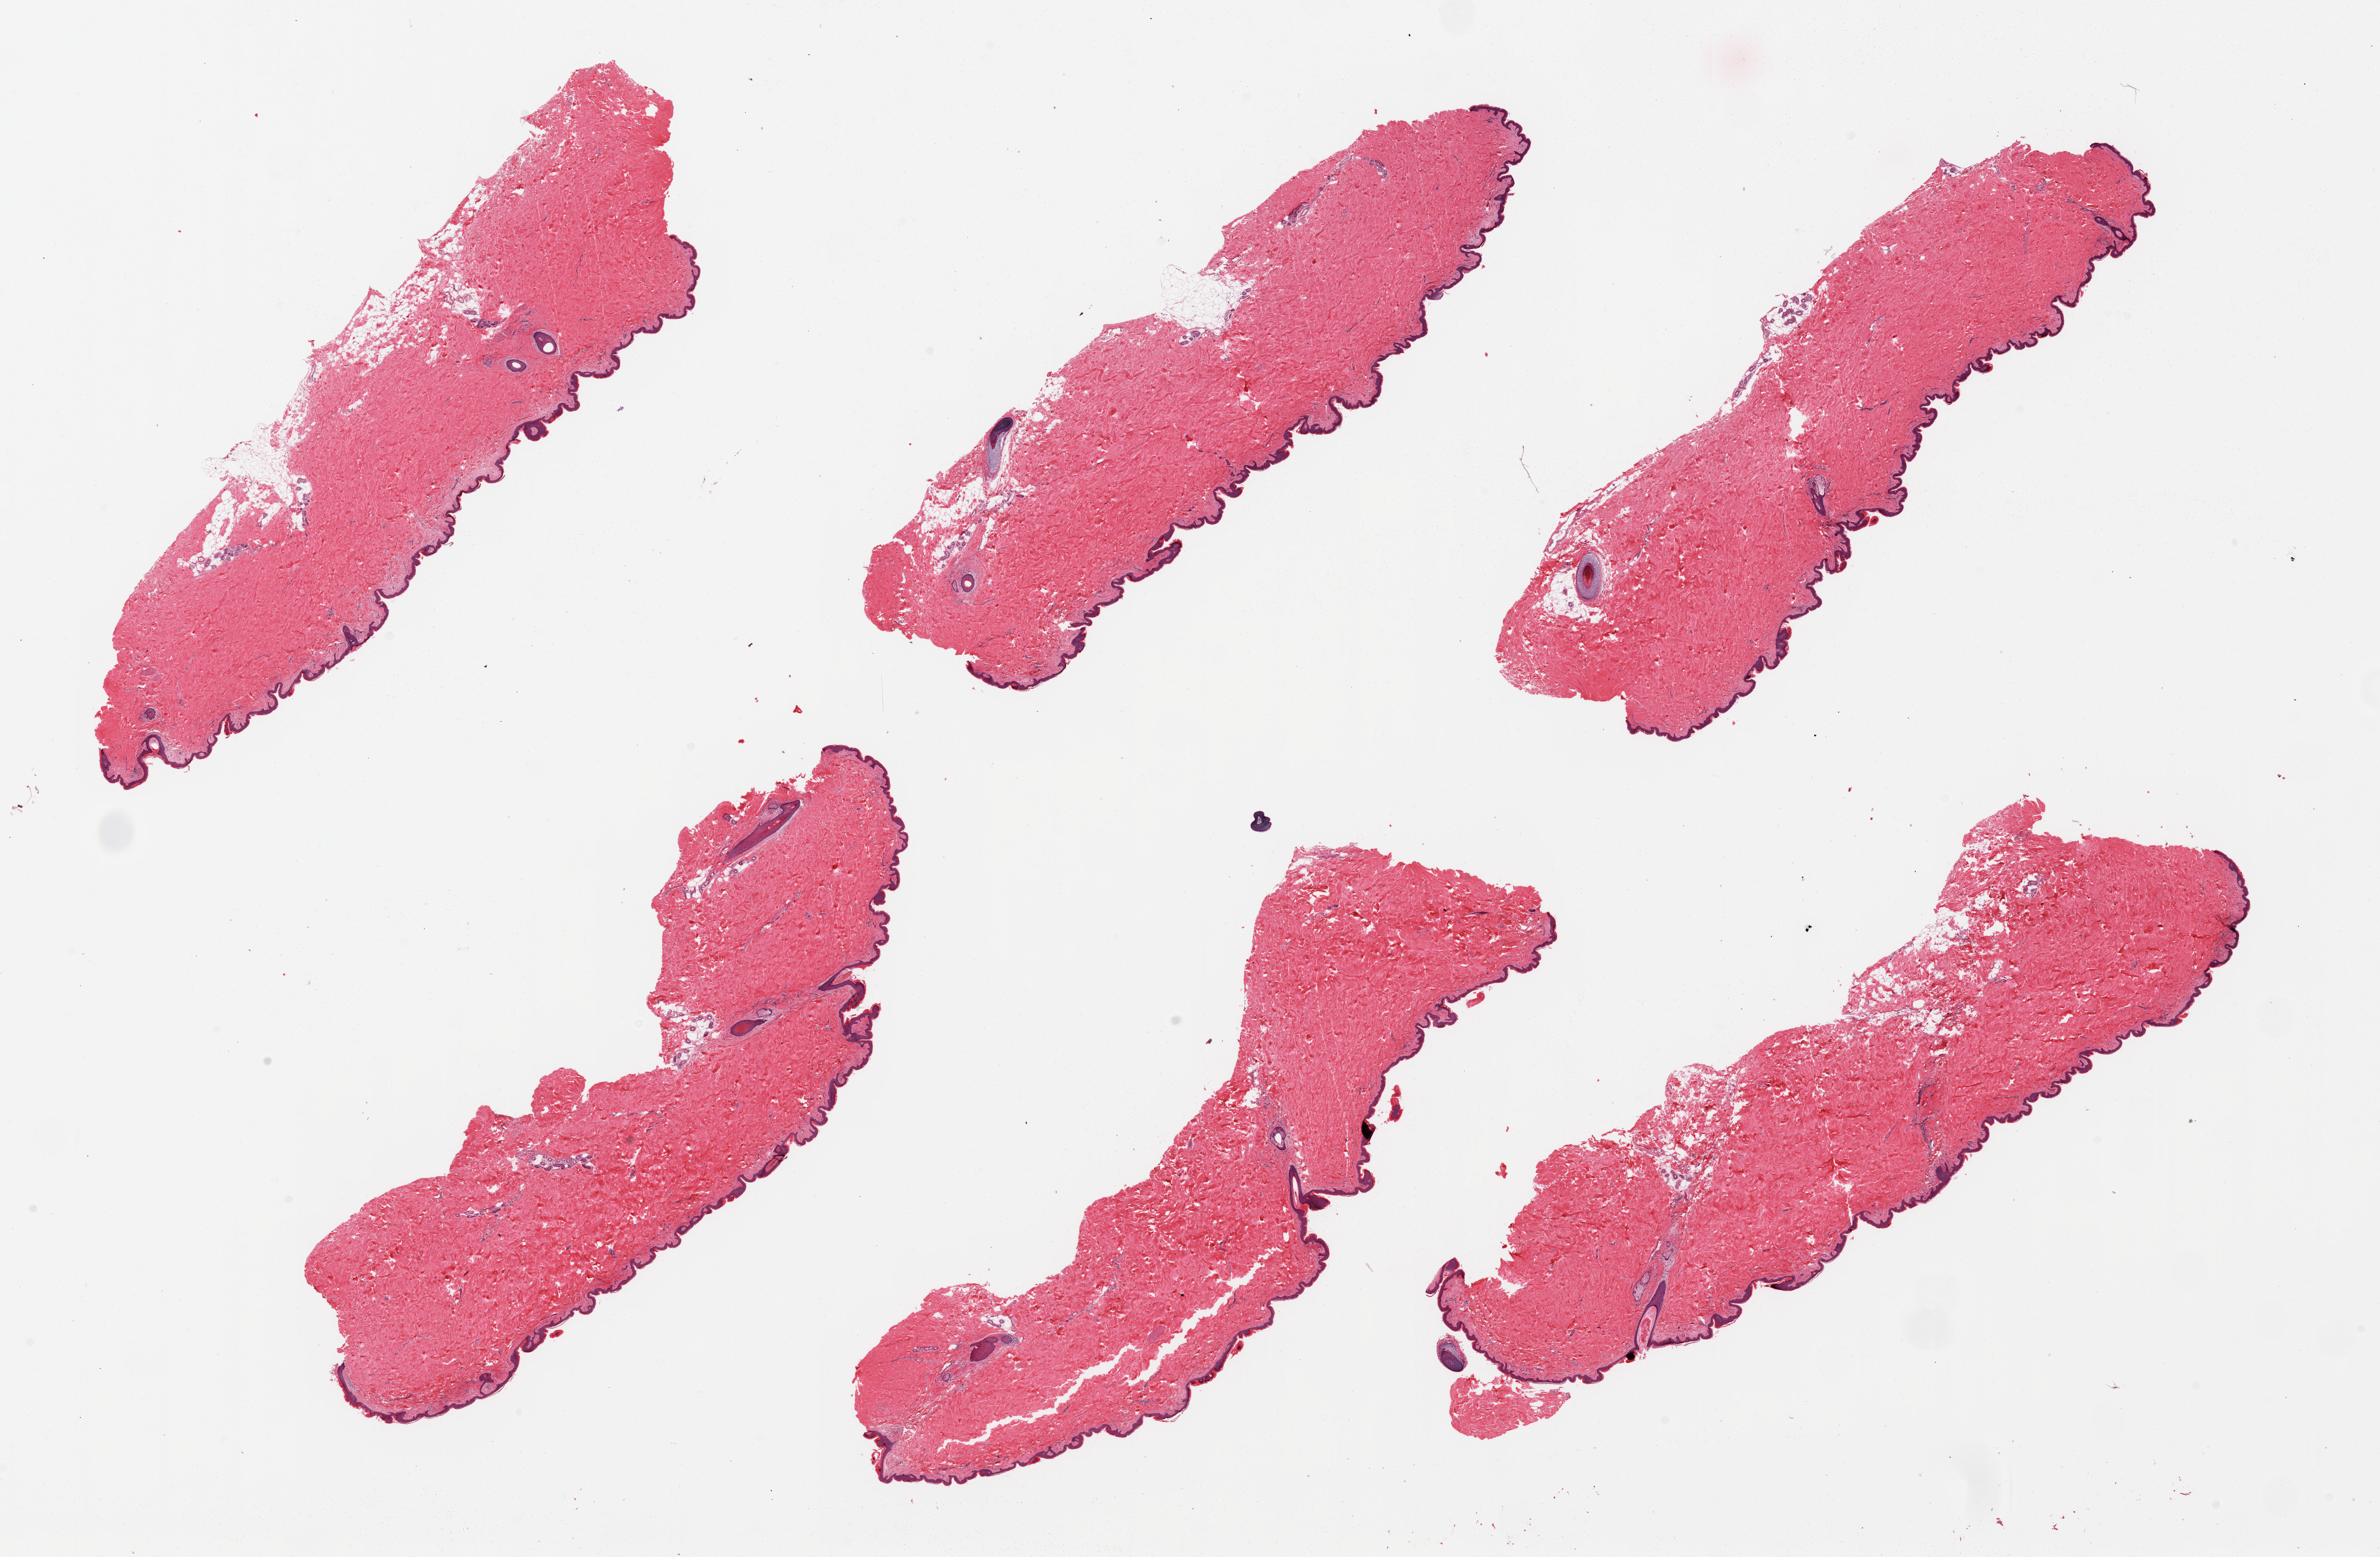
H&E whole-slide image, low-resolution overview of the scanned area, about 31.5 x 20.6 mm. PAXgene-fixed, paraffin-embedded tissue. Sampled site (target tissue): skin of suprapubic region. Donor tissue sample. Donor sex: male.
• pathologist's review note for this sample: 6 pieces; well trimmed; <10% intradermal fat